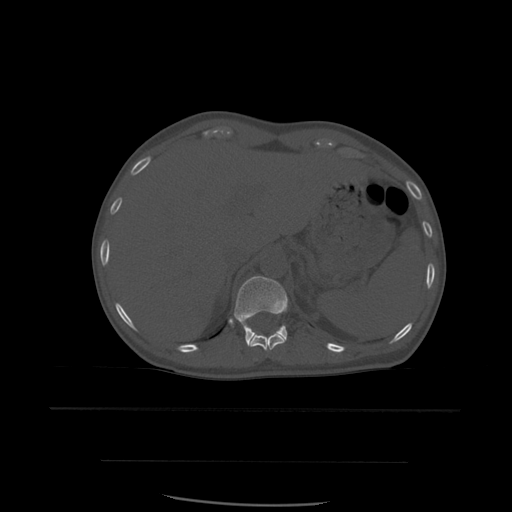
CT including the spine, one axial slice. Position 285 of 574 along the scan axis. Bone window (W 1800 / L 400 HU). 1.25 mm slice thickness. 512 × 512 image matrix, field of view 392 × 392 mm. Patient age 48 years. From the clinical record (not read from this slice): primary cancer: lung; vertebrae with lytic lesions (as recorded): T11.
Structures marked on this image (semi-automatic segmentation, software-assisted and operator-edited):
- T11 vertebra: bounding box <250,332,286,351> (left, top, right, bottom; pixels)
- T12 vertebra: <233,276,288,347>